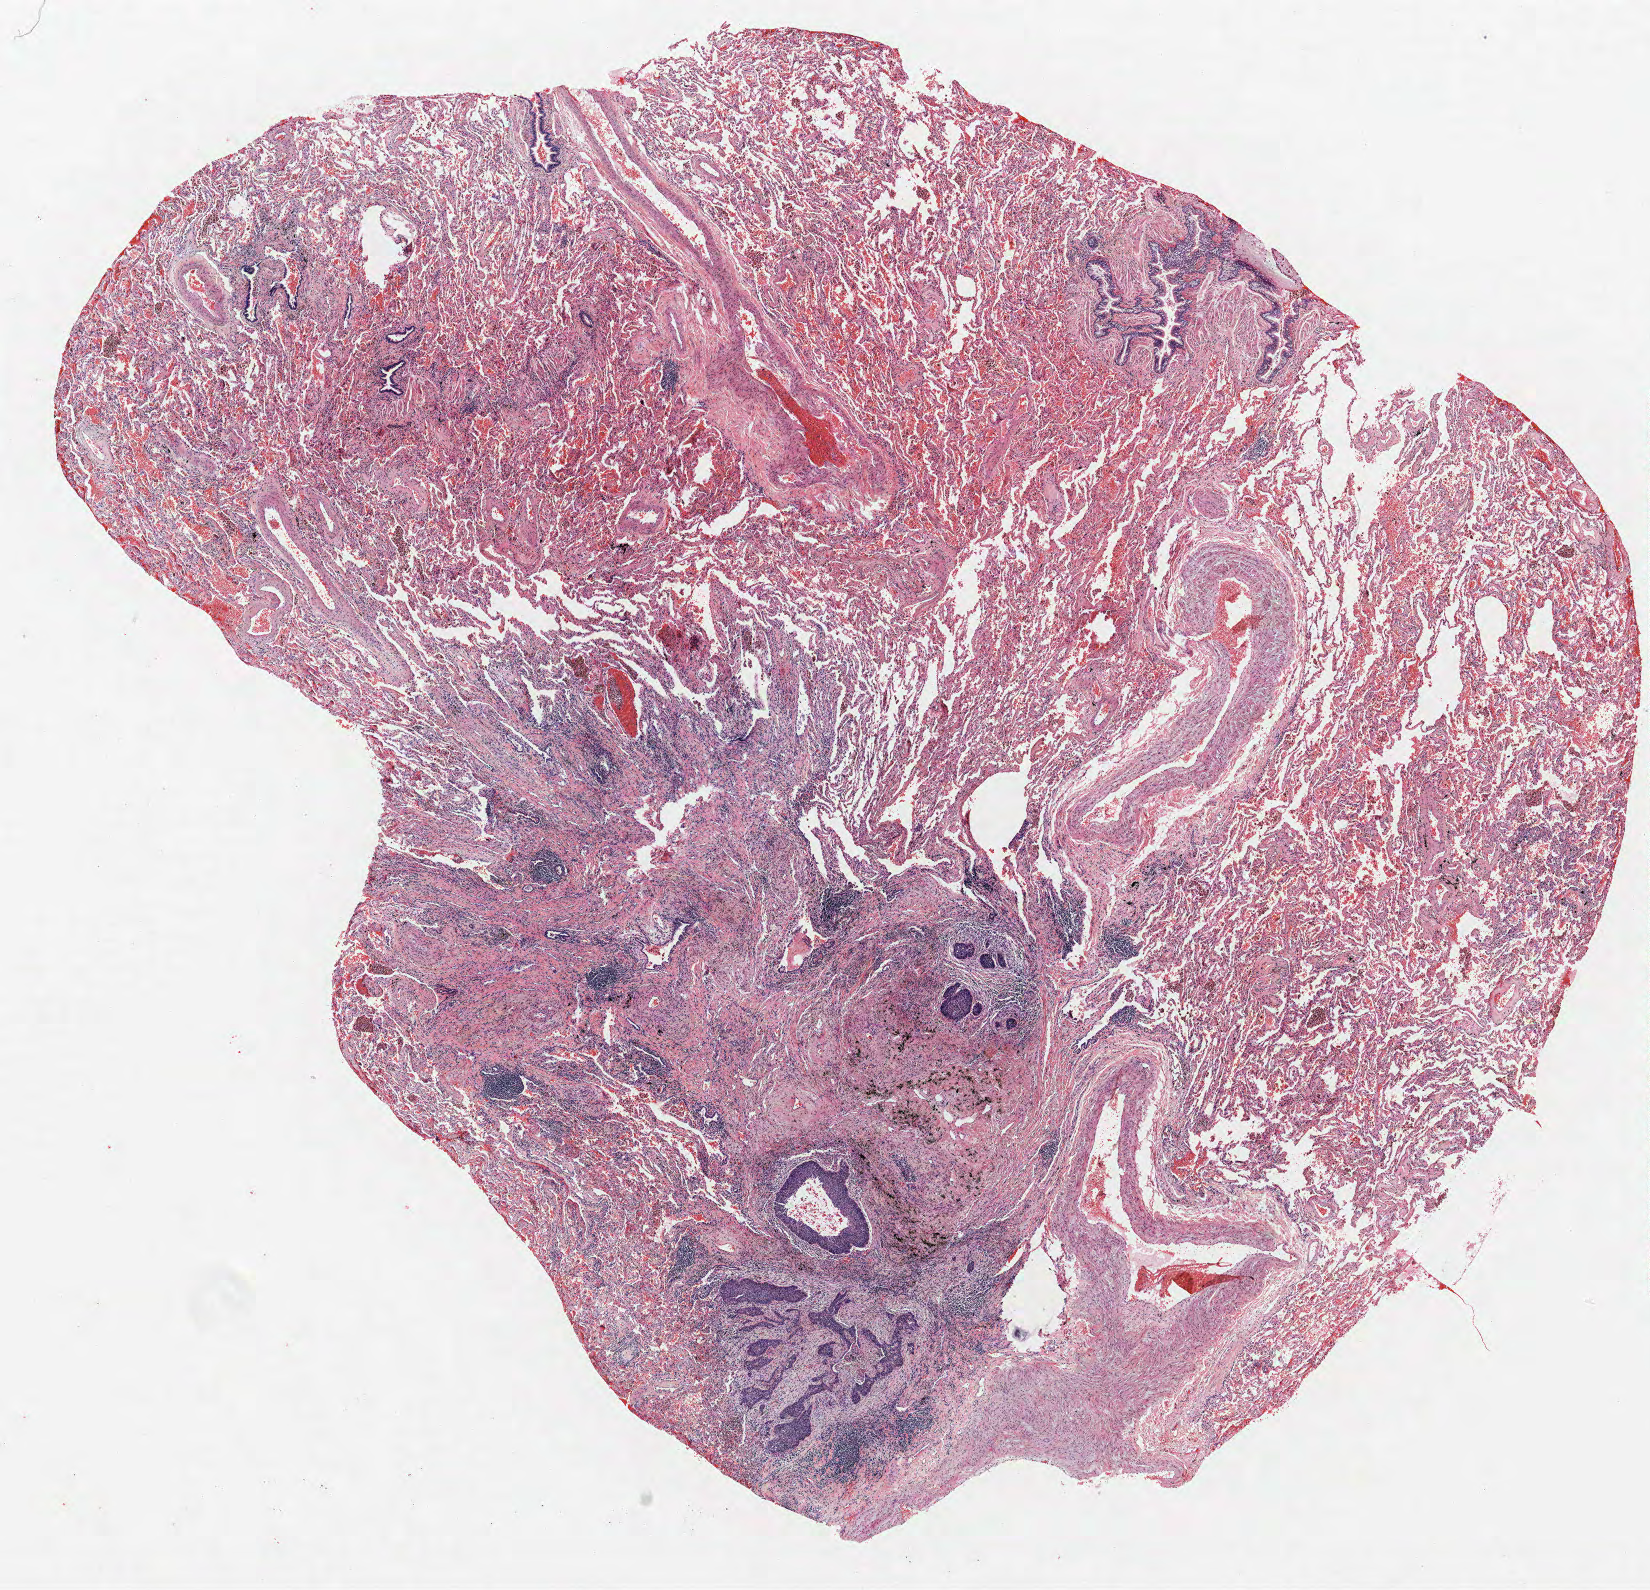
Hematoxylin and eosin (H&E) stained whole-slide image, a low-resolution overview of the entire scanned area, about 13.2 x 12.7 mm (slide scanned at 40x), formalin-fixed paraffin-embedded (FFPE) section, lung tissue. Female, age 71 at enrolment. Current smoker at enrolment. Grade: poorly differentiated (G3).
Stage (AJCC 6th edition): IA. Tumour size (pathology): 8 mm. Primary tumour location (clinical record): right lower lobe. Participant's lung-cancer diagnosis: Squamous cell carcinoma, NOS.